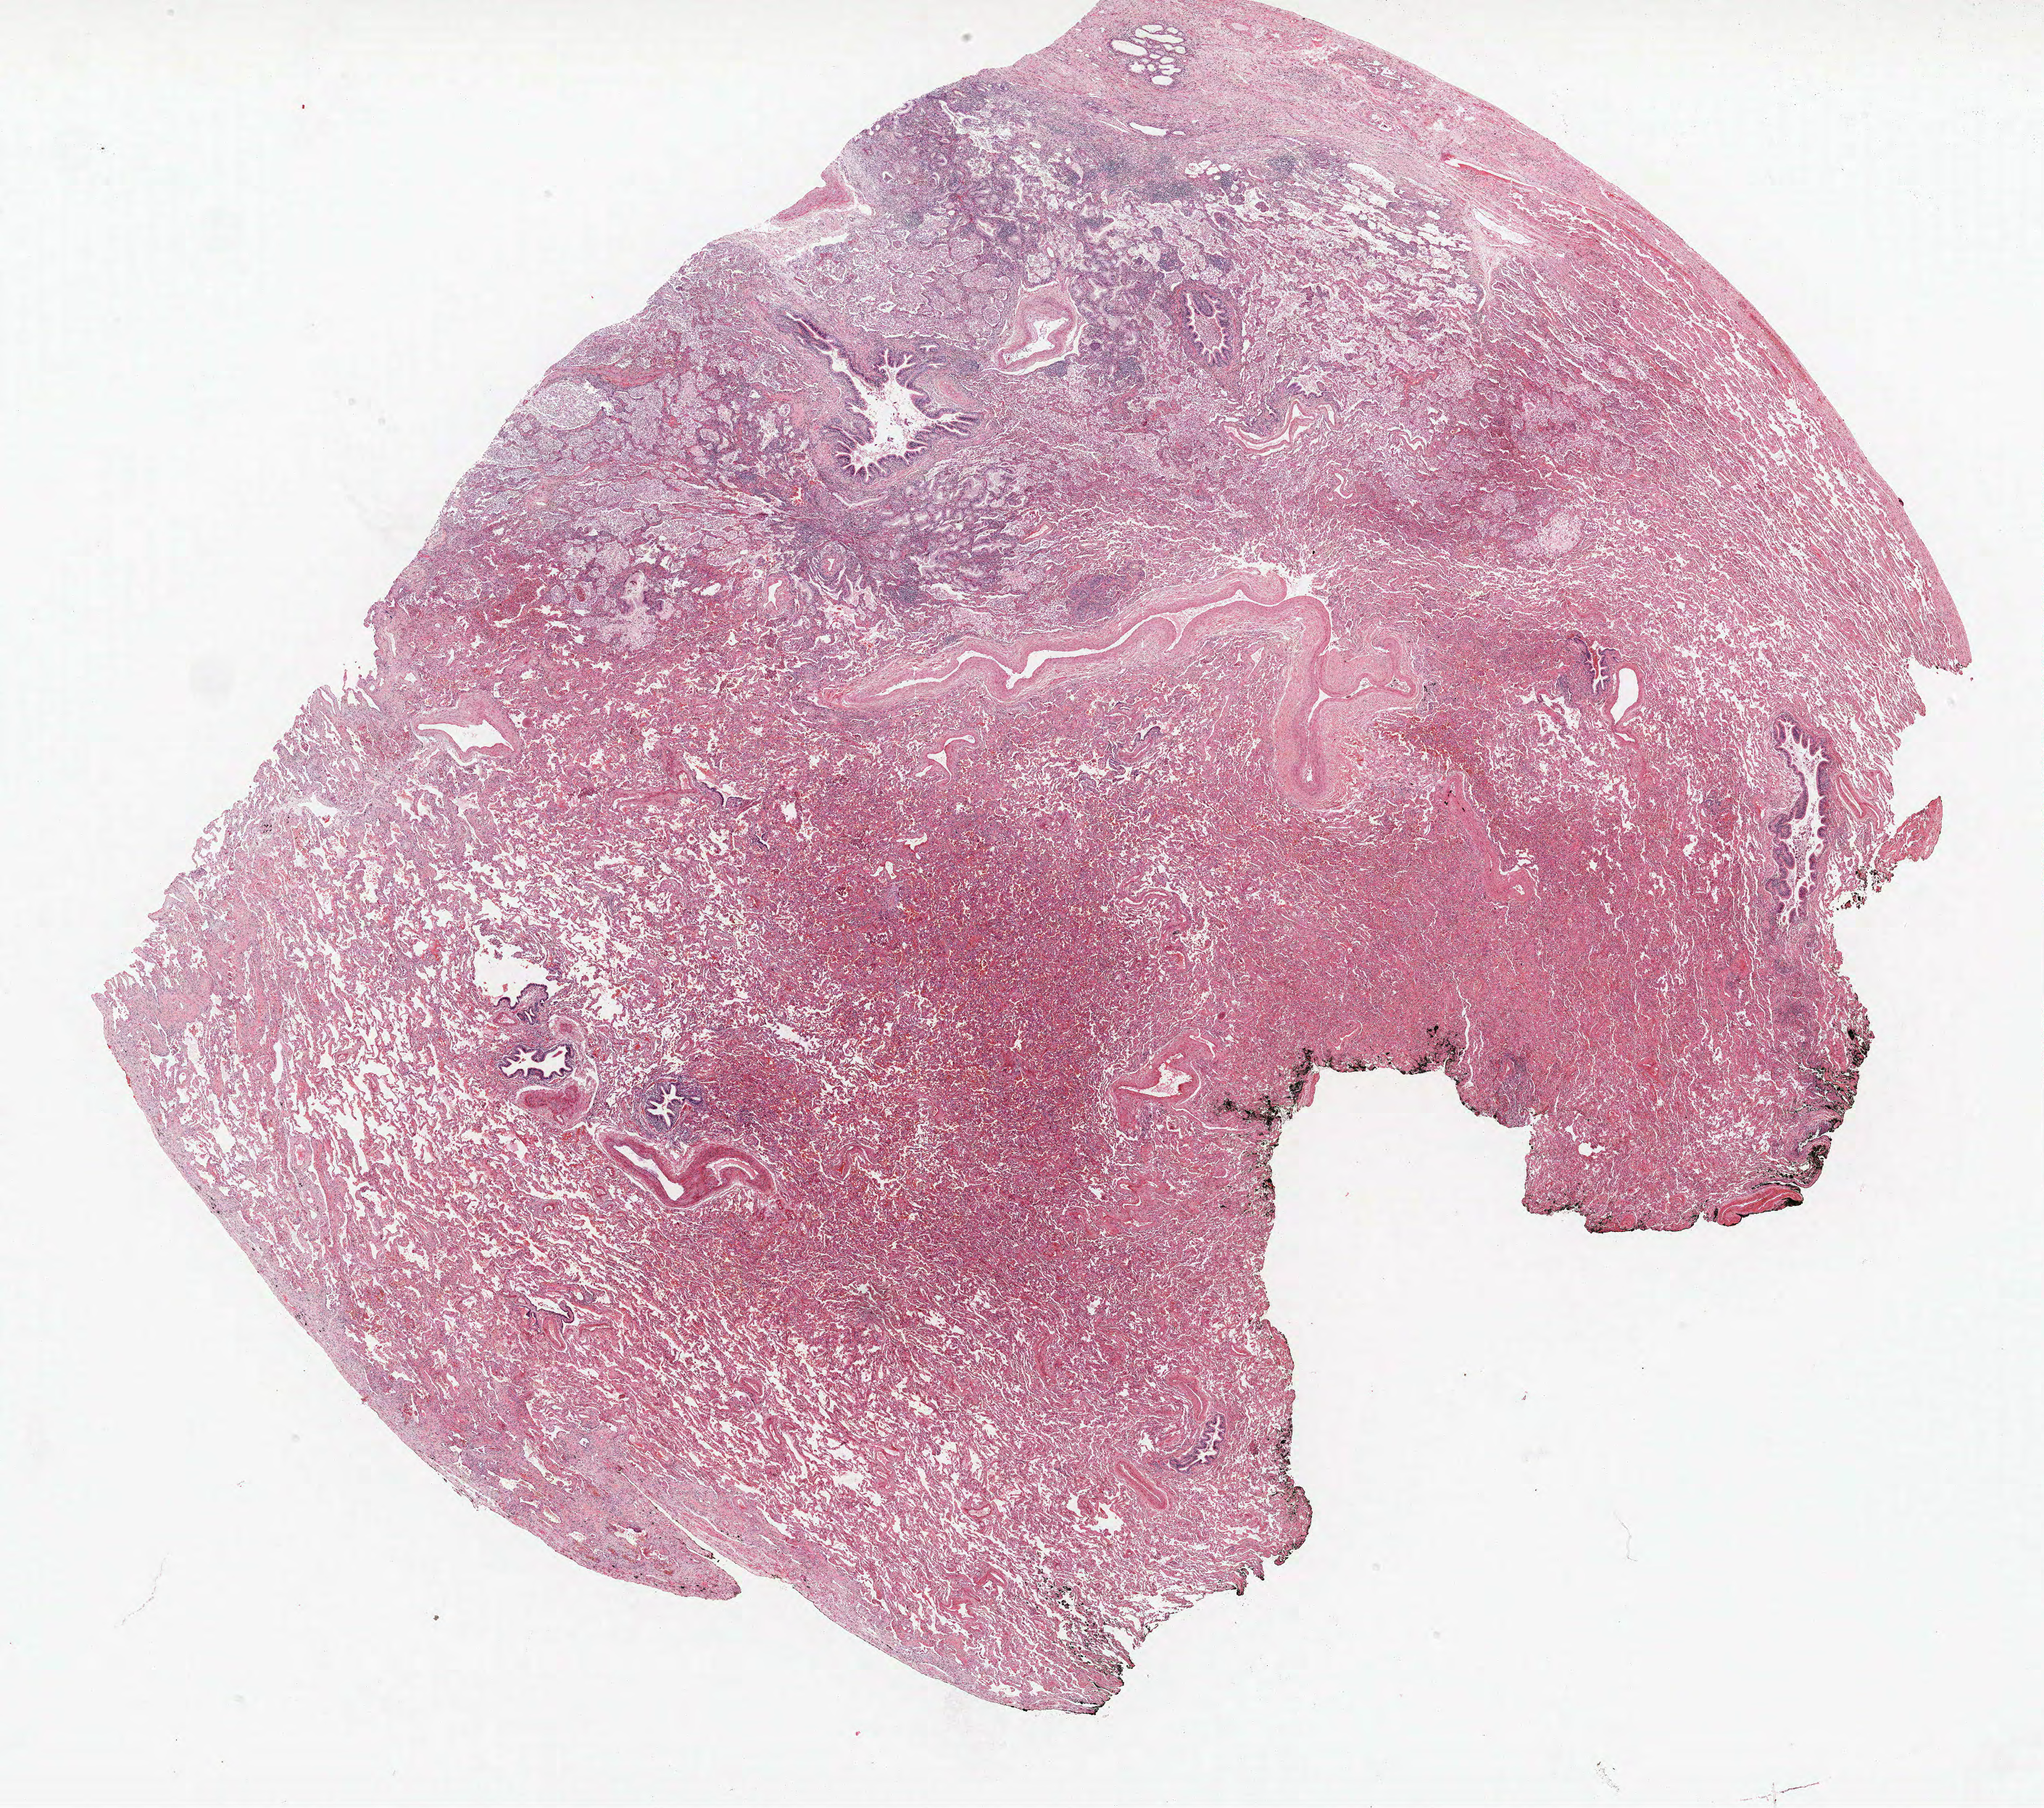
Whole-slide histology image, H&E-stained, whole scanned area (about 22.6 x 20.0 mm, acquisition: 40x scan) shown as a low-resolution overview, formalin-fixed paraffin-embedded (FFPE) section, lung. Female patient, aged 59 at enrolment. Former smoker at enrolment. Grade: well differentiated (G1).
* tumour size (pathology): 15 mm
* primary tumour location (clinical record): right lower lobe
* stage (AJCC 6th edition): IA
* participant's lung-cancer diagnosis: Bronchiolo-alveolar carcinoma, mucinous
* ICD-O-3 topography: lower lobe of lung (C34.3)